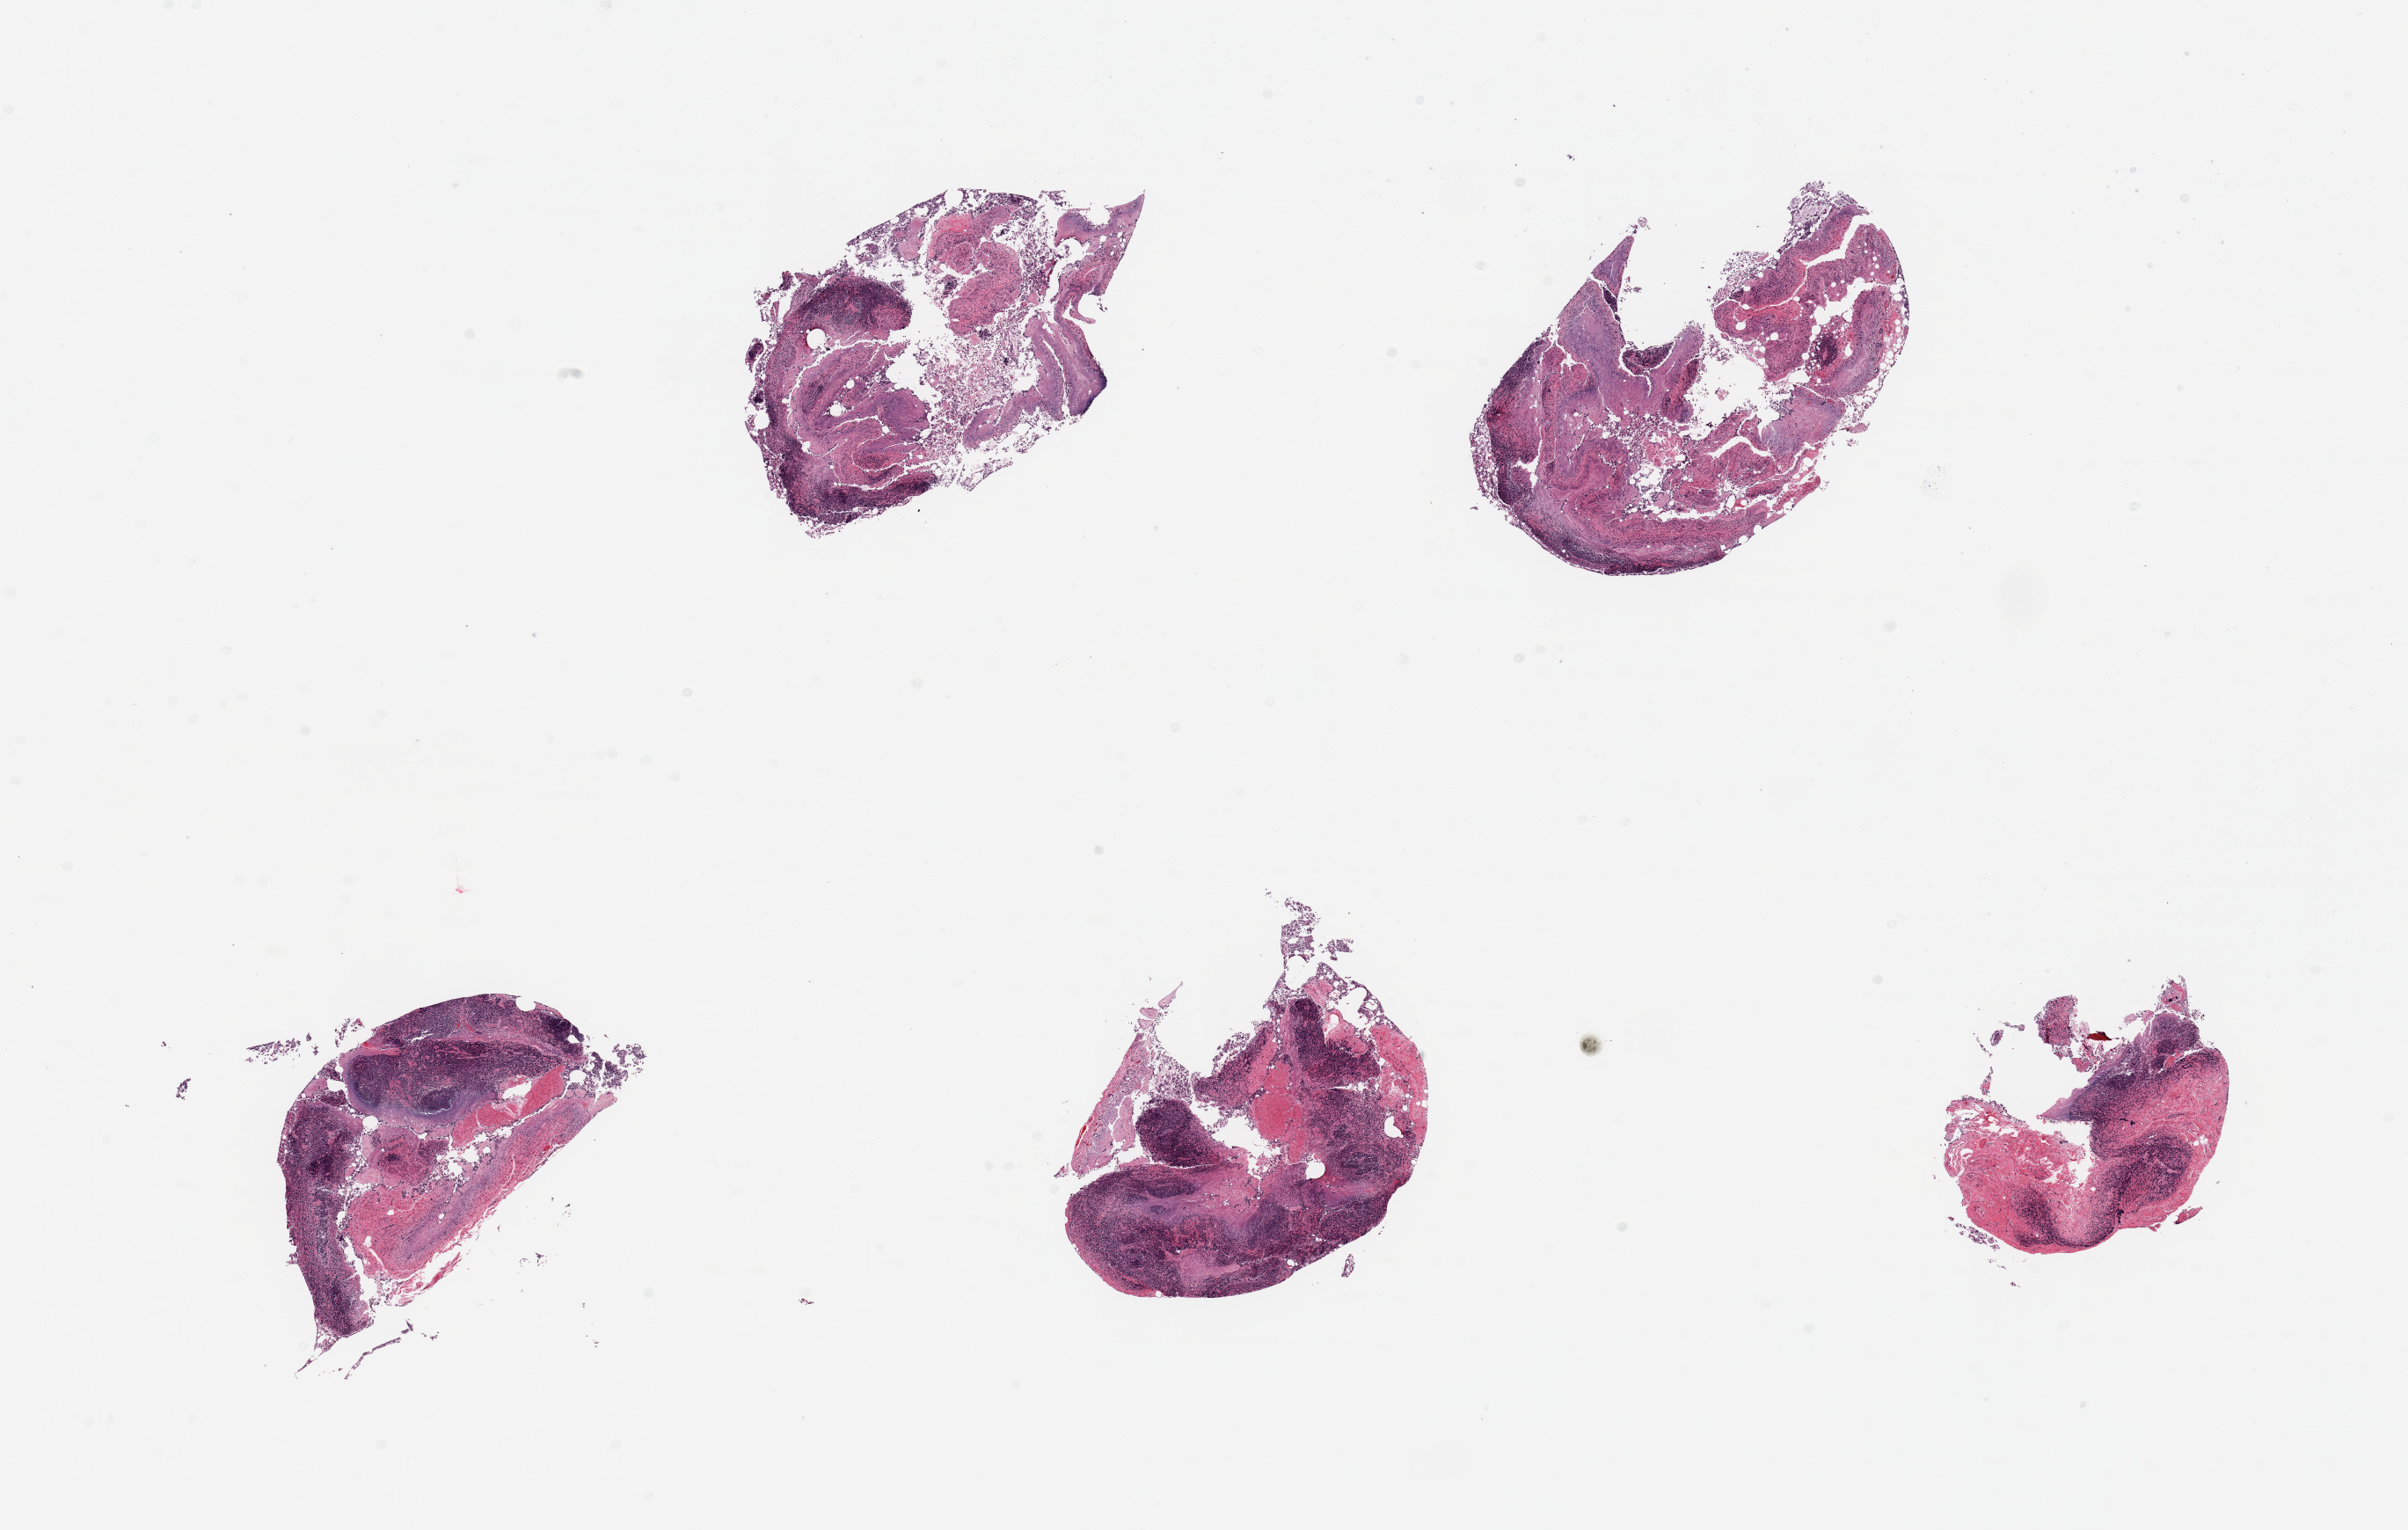
Hematoxylin and eosin (H&E) whole-slide image — whole scanned area (about 21.7 x 13.8 mm) shown as a low-resolution overview. PAXgene-fixed, paraffin-embedded tissue. Target tissue: ileum. Donor tissue sample. Donor: male.
• pathologist's review note for this sample: 5 pieces; abundant lymphoid tissue with equal amounts of autolyzed ileum